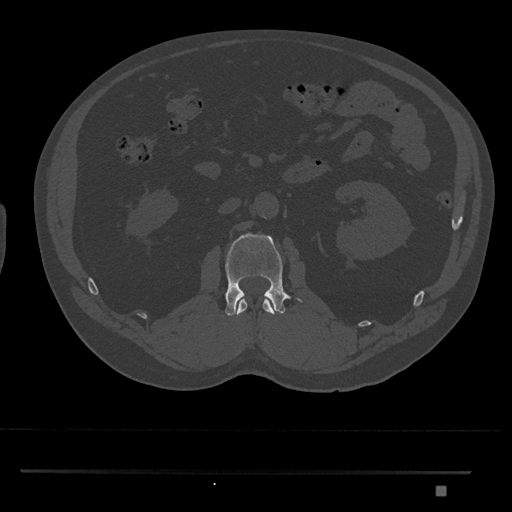
CT including the spine, one axial slice. Reconstruction kernel Br40s/3. 120 kVp. Bone window (W 1800 / L 400 HU). 512 × 512 image matrix, field of view 429 × 429 mm. Patient: male, 65 years. Case-level facts recorded for this patient, not image findings: primary cancer: prostate.
Outlined on this slice (semi-automatically segmented with operator editing):
- L1 vertebra: bounding box (x1, y1, x2, y2) in pixels: (236, 299, 275, 316)
- L2 vertebra: (225, 233, 302, 316)